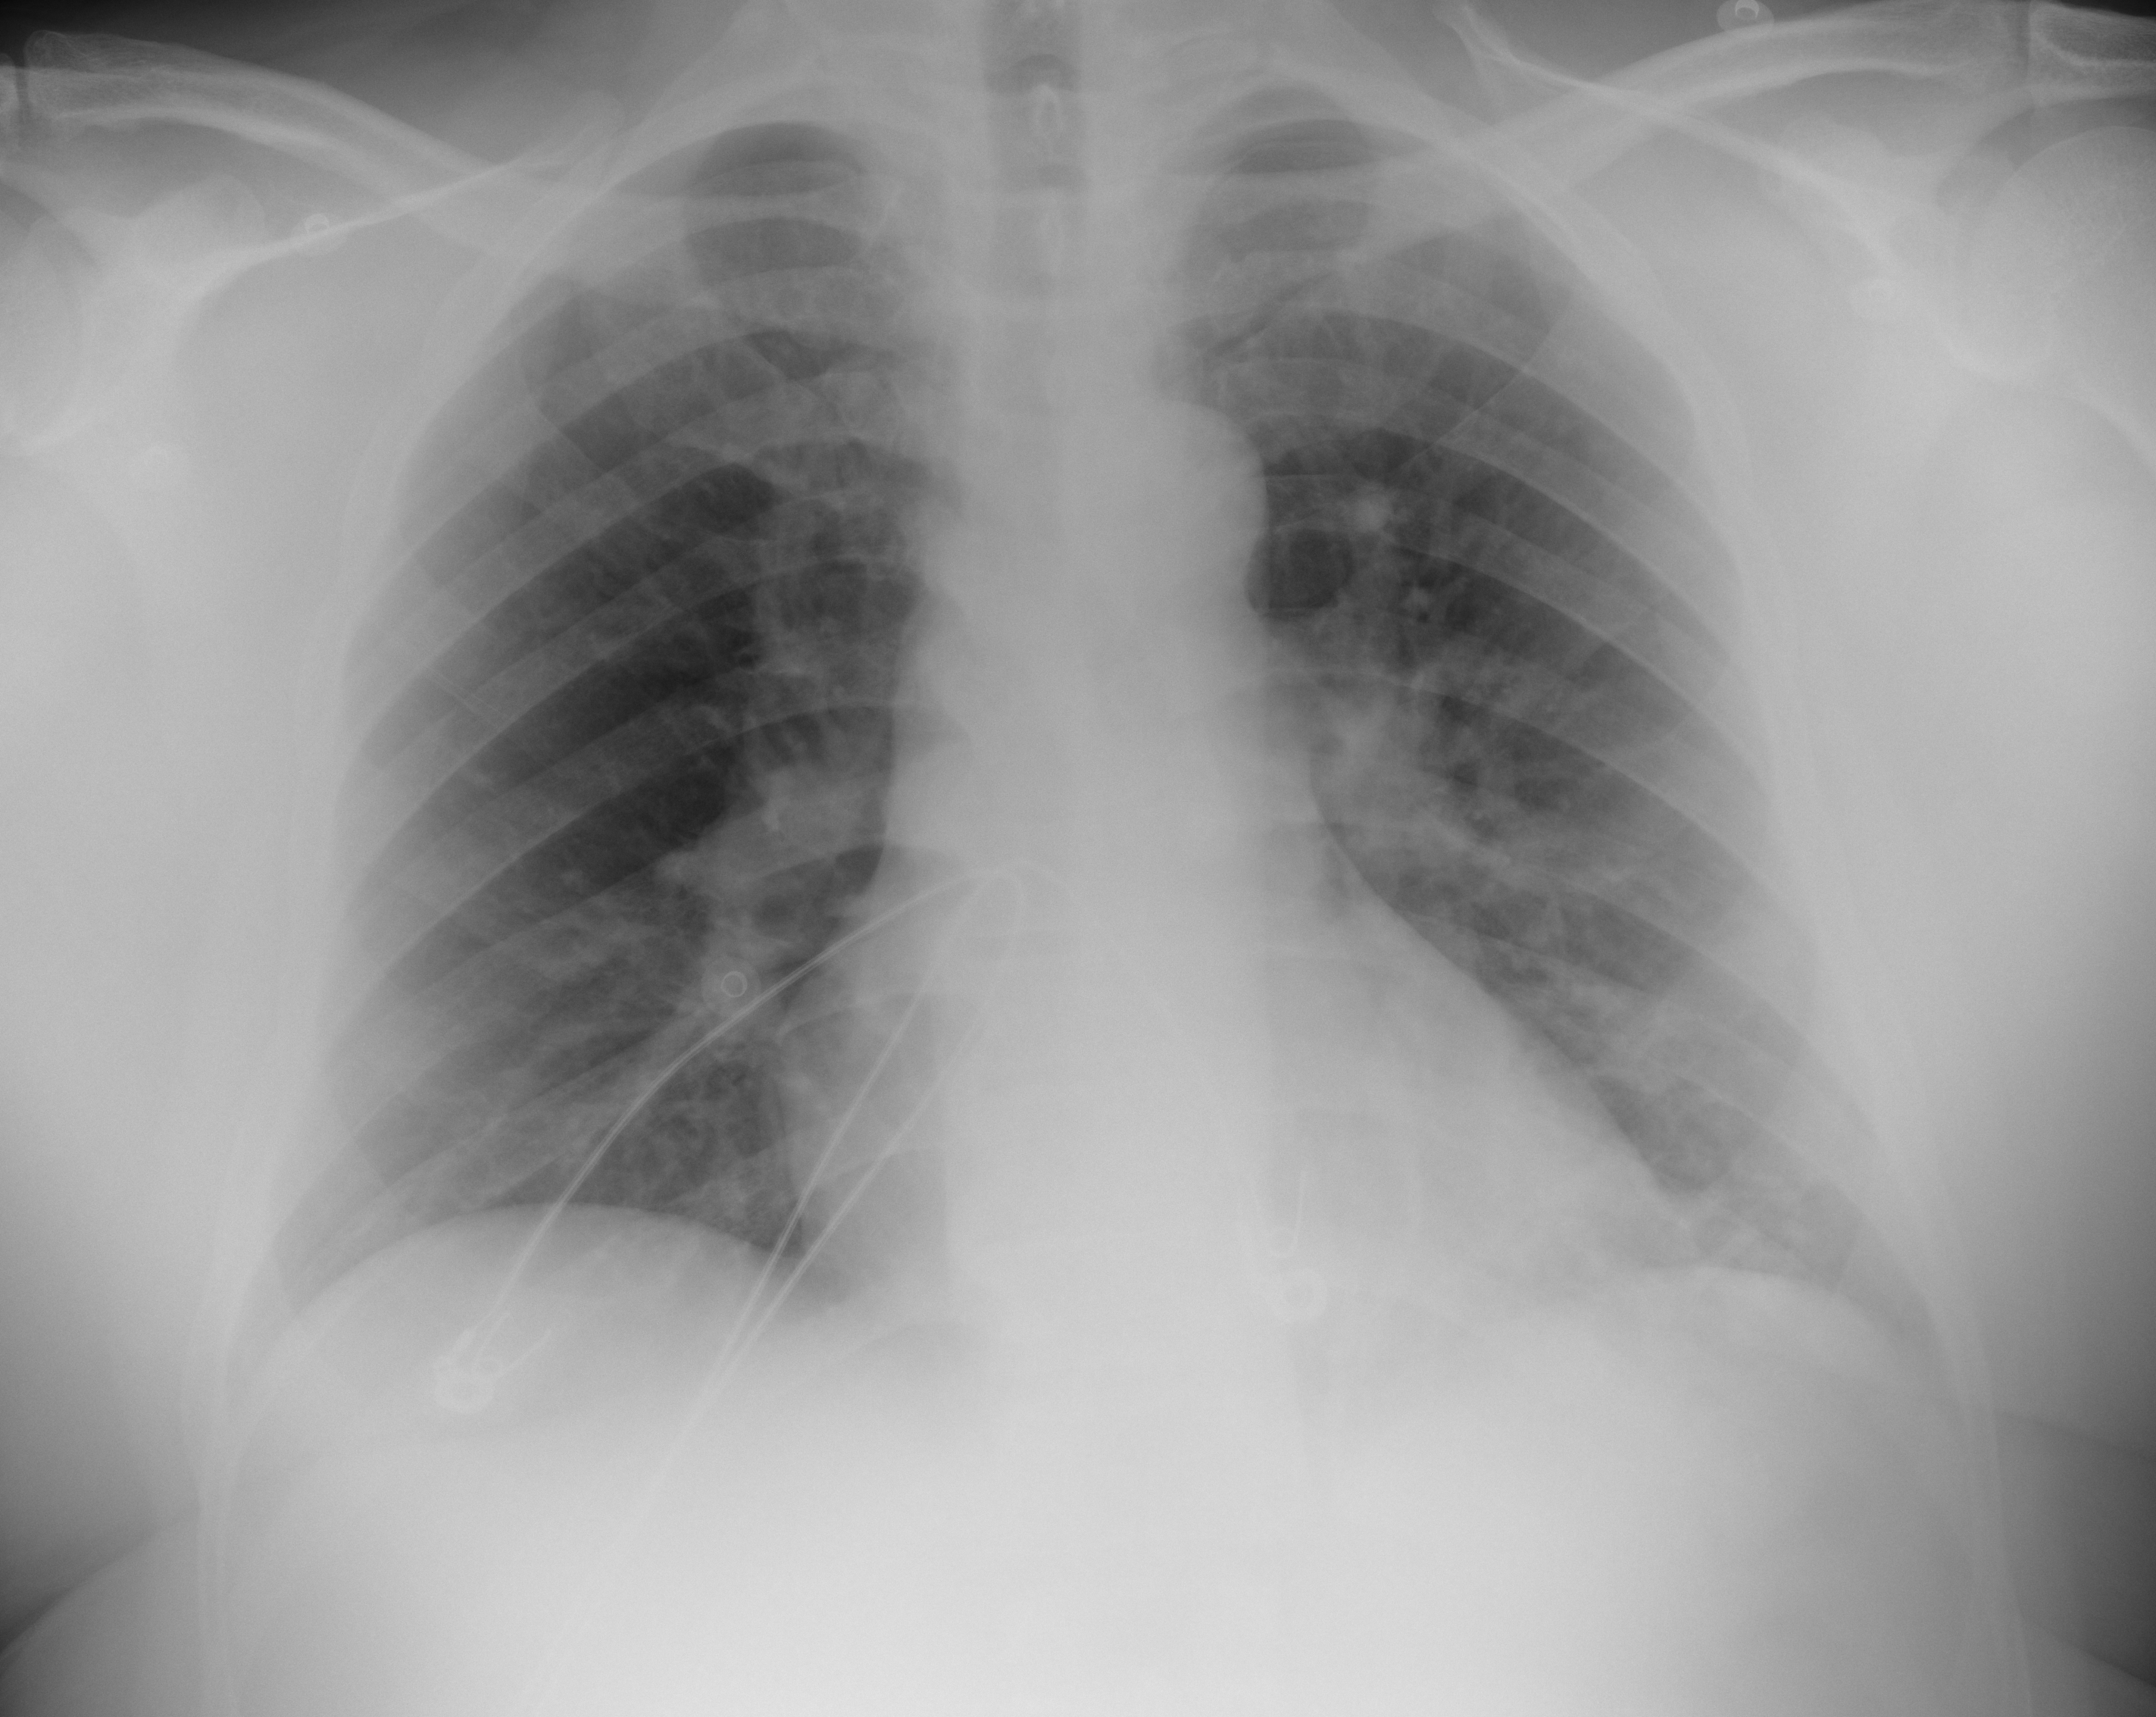
Portable chest radiograph, AP projection. Male patient, age 47 years; imaged 0 days after the COVID-19 diagnosis.
Radiologist's key findings for this exam: Ill-defined left lower lung airspace opacities.